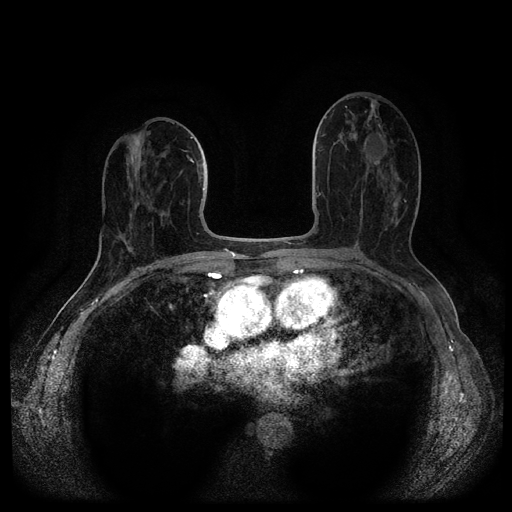
Breast MRI (dynamic contrast-enhanced, multi-phase), one axial slice; slice 51 of 116 in the series (ordered by position); dynamic contrast-enhanced series, time point 2 of 5 at this slice position (early post-contrast); 1.5 T; TE 2.6 ms, TR 5.4 ms; 2.1 mm slice thickness; 512 × 512 image matrix, field of view 340 × 340 mm. Patient: female, 69 years.
Structures marked on this image (semi-automatic segmentation, software-assisted and operator-edited):
- breast lesion (labelled benign in the annotation): bounding box (x1, y1, x2, y2) in pixels: (363, 137, 388, 168)